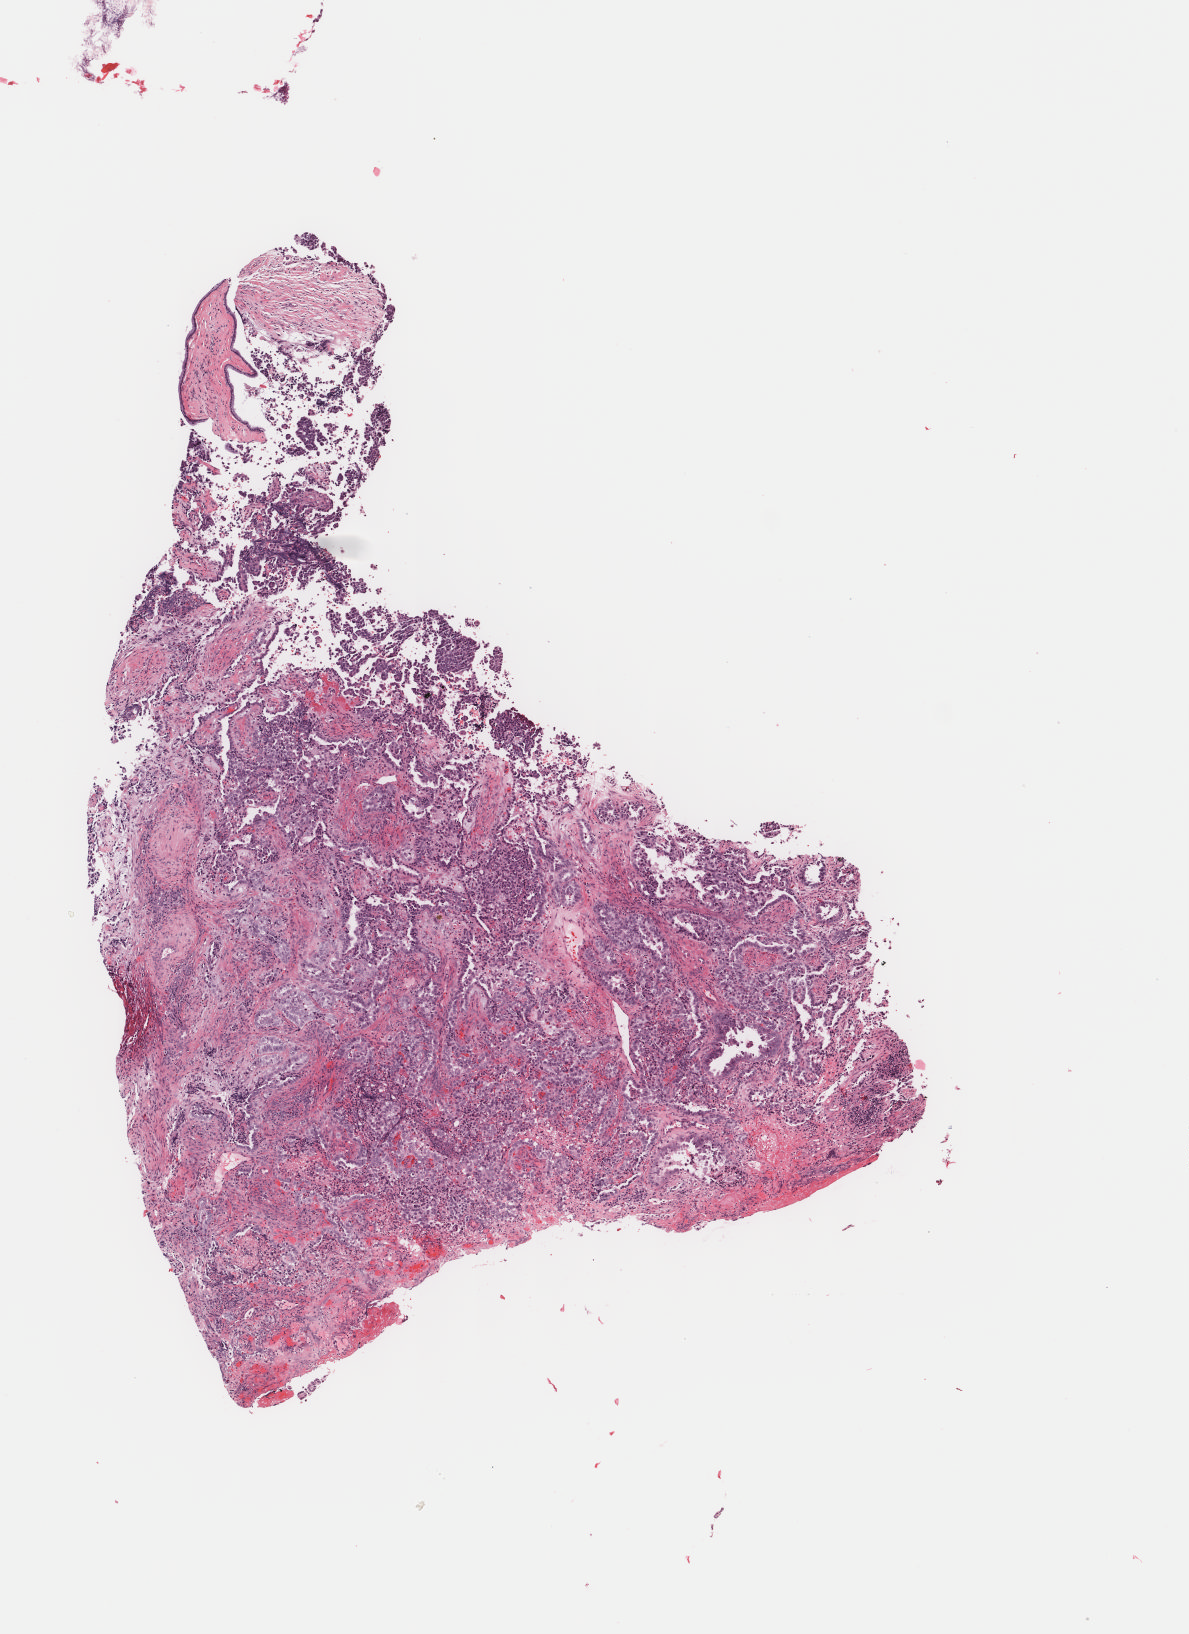
Whole-slide histology image, Hematoxylin and eosin (H&E) stained — shown as a low-resolution overview of the whole scanned area (about 4.7 x 6.5 mm, from a 40x scan); frozen section; sample: primary tumour, uterus. Female, age 69 years at initial diagnosis. Histologic grade: G3 (poorly differentiated). Pathologist review of this section (percent, as recorded): tumour cells 100%, tumour nuclei 60%, normal cells 0%, stromal cells 0%, necrosis 0%. Inflammatory infiltration, as recorded: lymphocyte infiltration 4%, monocyte infiltration 0%, neutrophil infiltration 2%.
Diagnosis: Serous cystadenocarcinoma, NOS (endometrium). FIGO stage: IIIC.